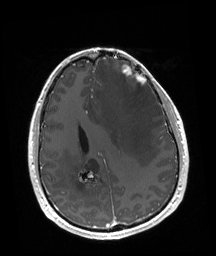
Brain MRI from a brain-tumour surgery series, one axial slice; slice 67 of 192 in the series (ordered by position); T1-weighted post-contrast; 216 × 256 image matrix, field of view 219 × 260 mm.
Structures marked on this image (outlined manually by an expert reader):
- tumour: bounding box [x1, y1, x2, y2] px = [121, 65, 146, 88]